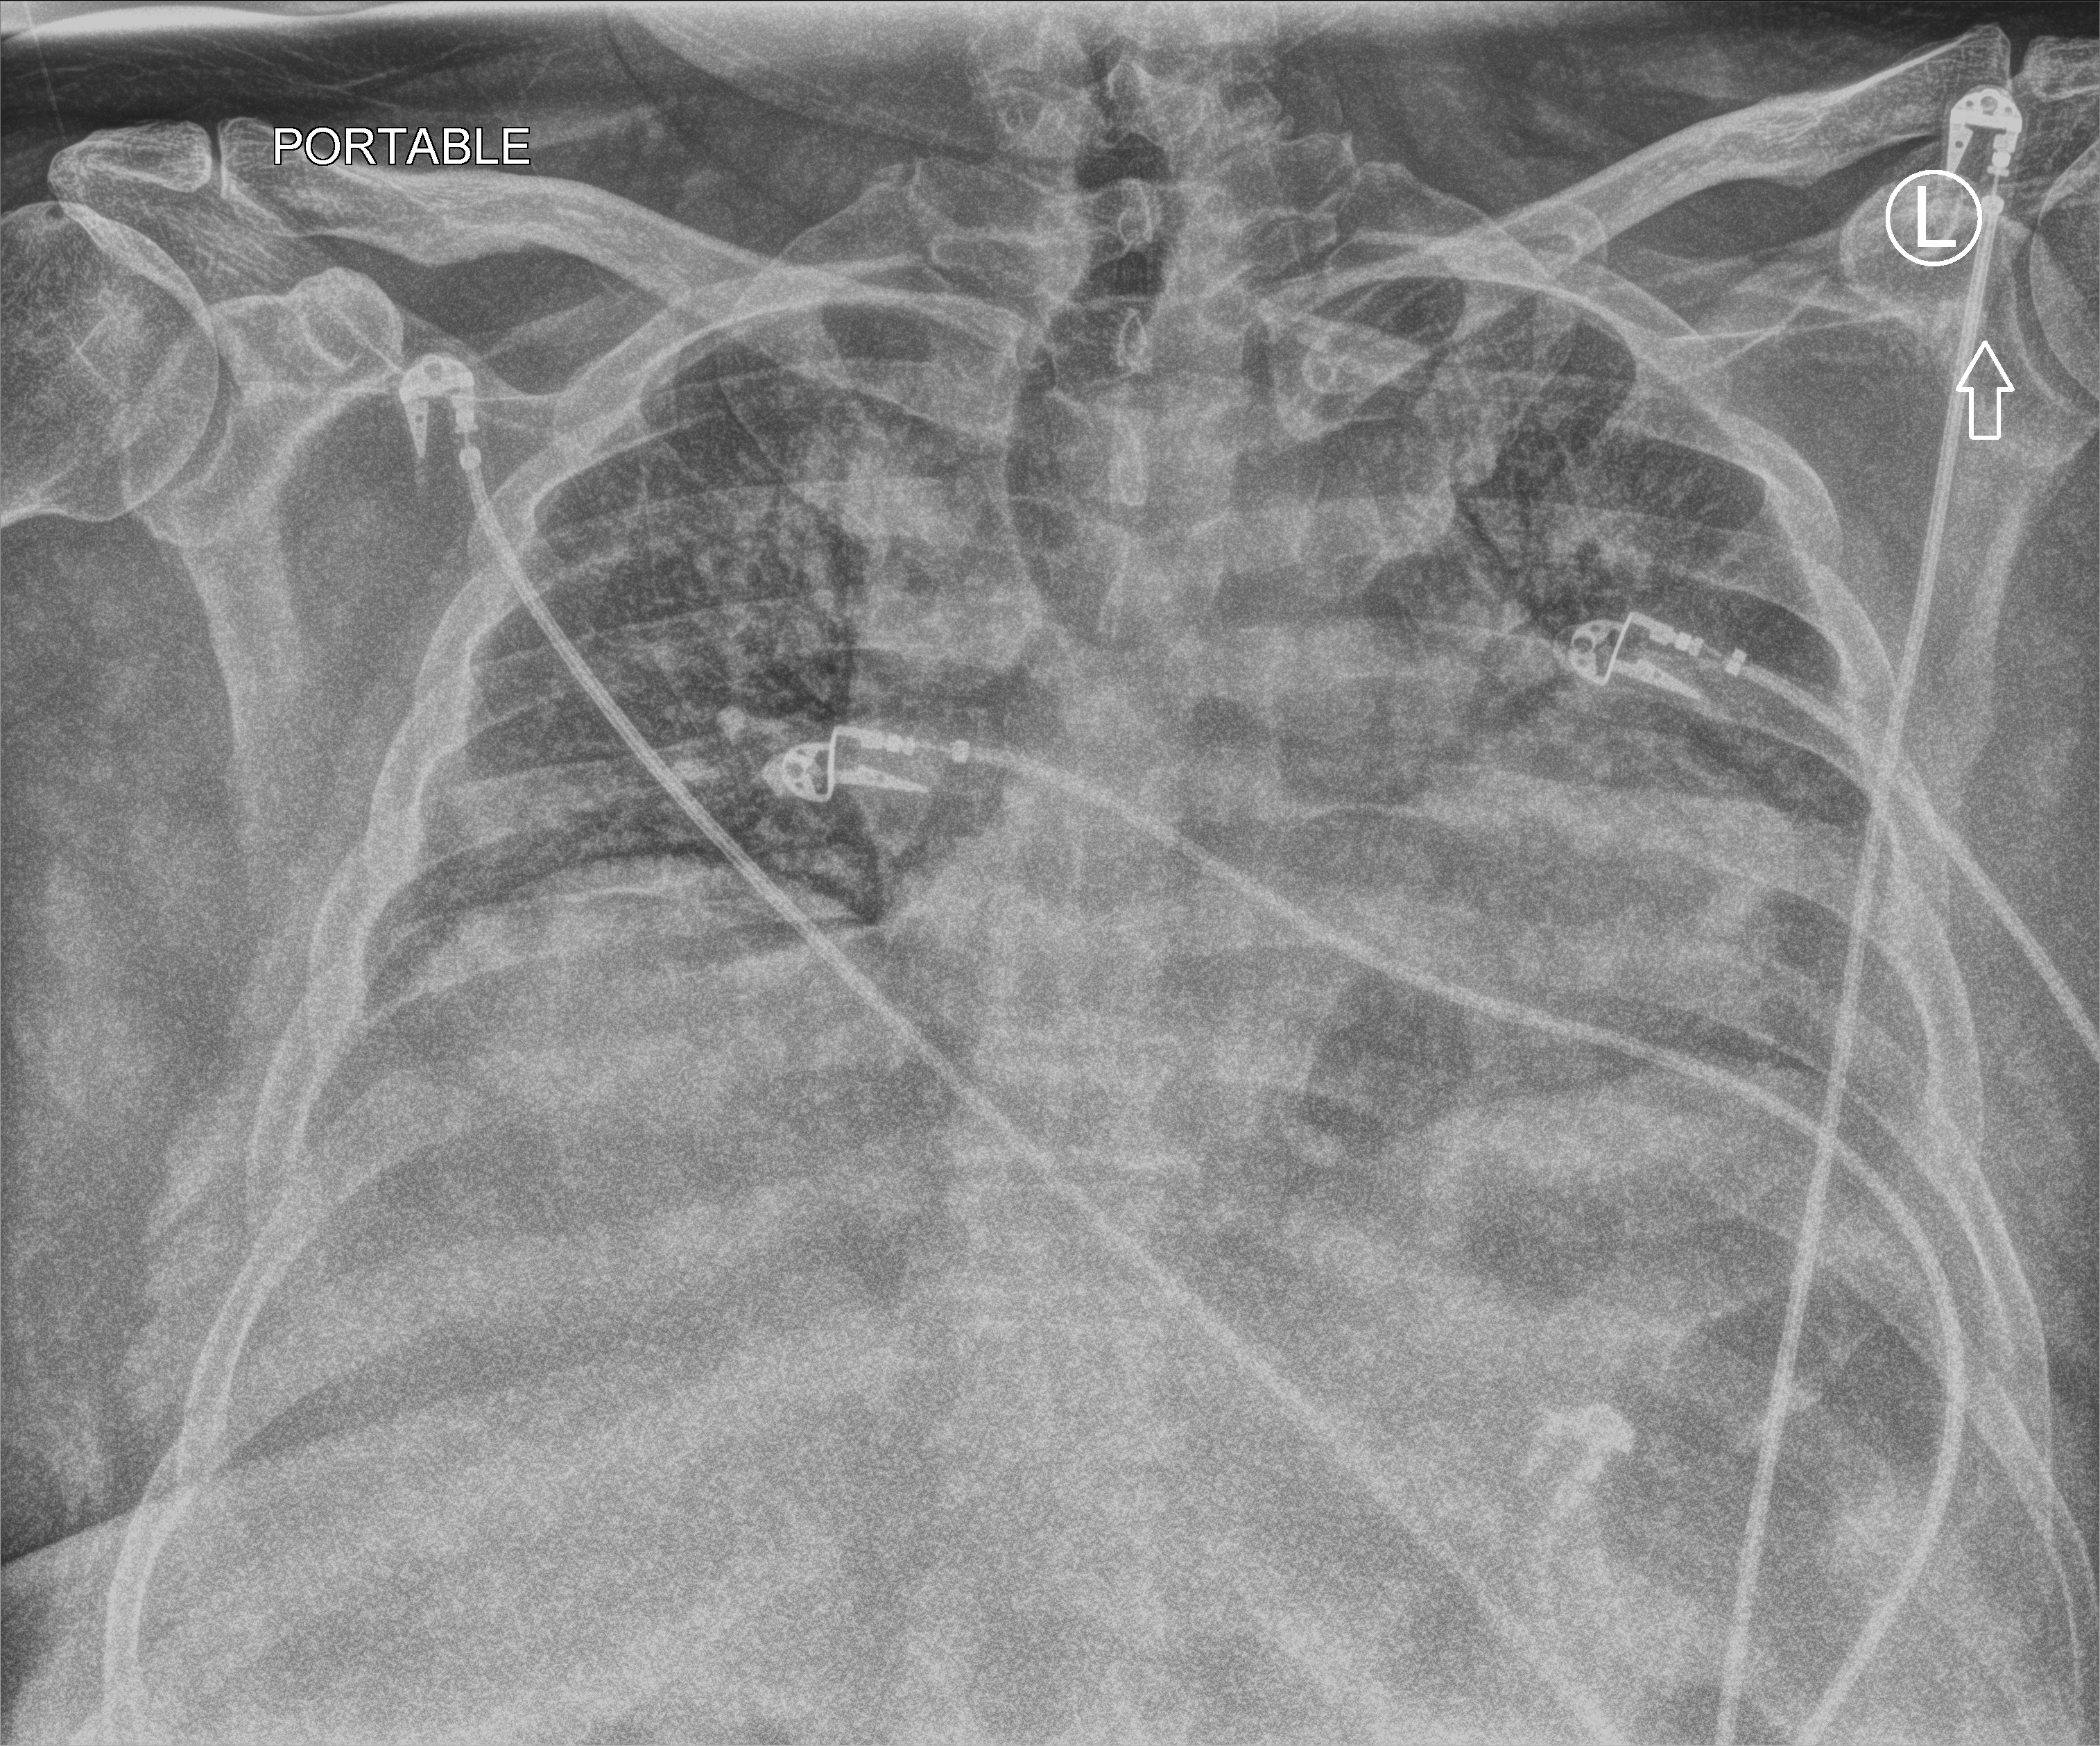
Bedside chest radiograph (computed radiography); anteroposterior (AP) projection. Patient hospitalised with COVID-19, aged 18–59 years.
From the hospital-stay record, not from the radiograph (when in the stay this image was taken is not recorded): diabetes (admission record): yes; mechanically ventilated during this hospital stay: yes.